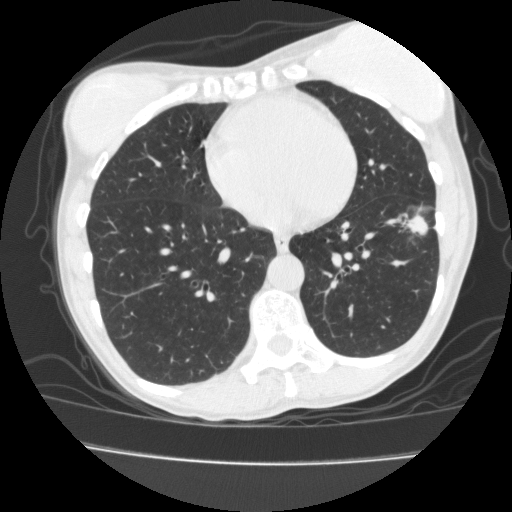
Low-dose screening chest CT, one axial slice. Position 64 of 171 along the scan axis. Reconstruction kernel FC10. 120 kVp. Lung window (W 1500 / L -600 HU). 2 mm slice thickness. 512 × 512 image matrix.
Outlined on this slice (expert manual segmentation):
- lesion 1 (tumor, lower lobe of left lung): bounding box (x1, y1, x2, y2) in pixels: (406, 216, 427, 234)